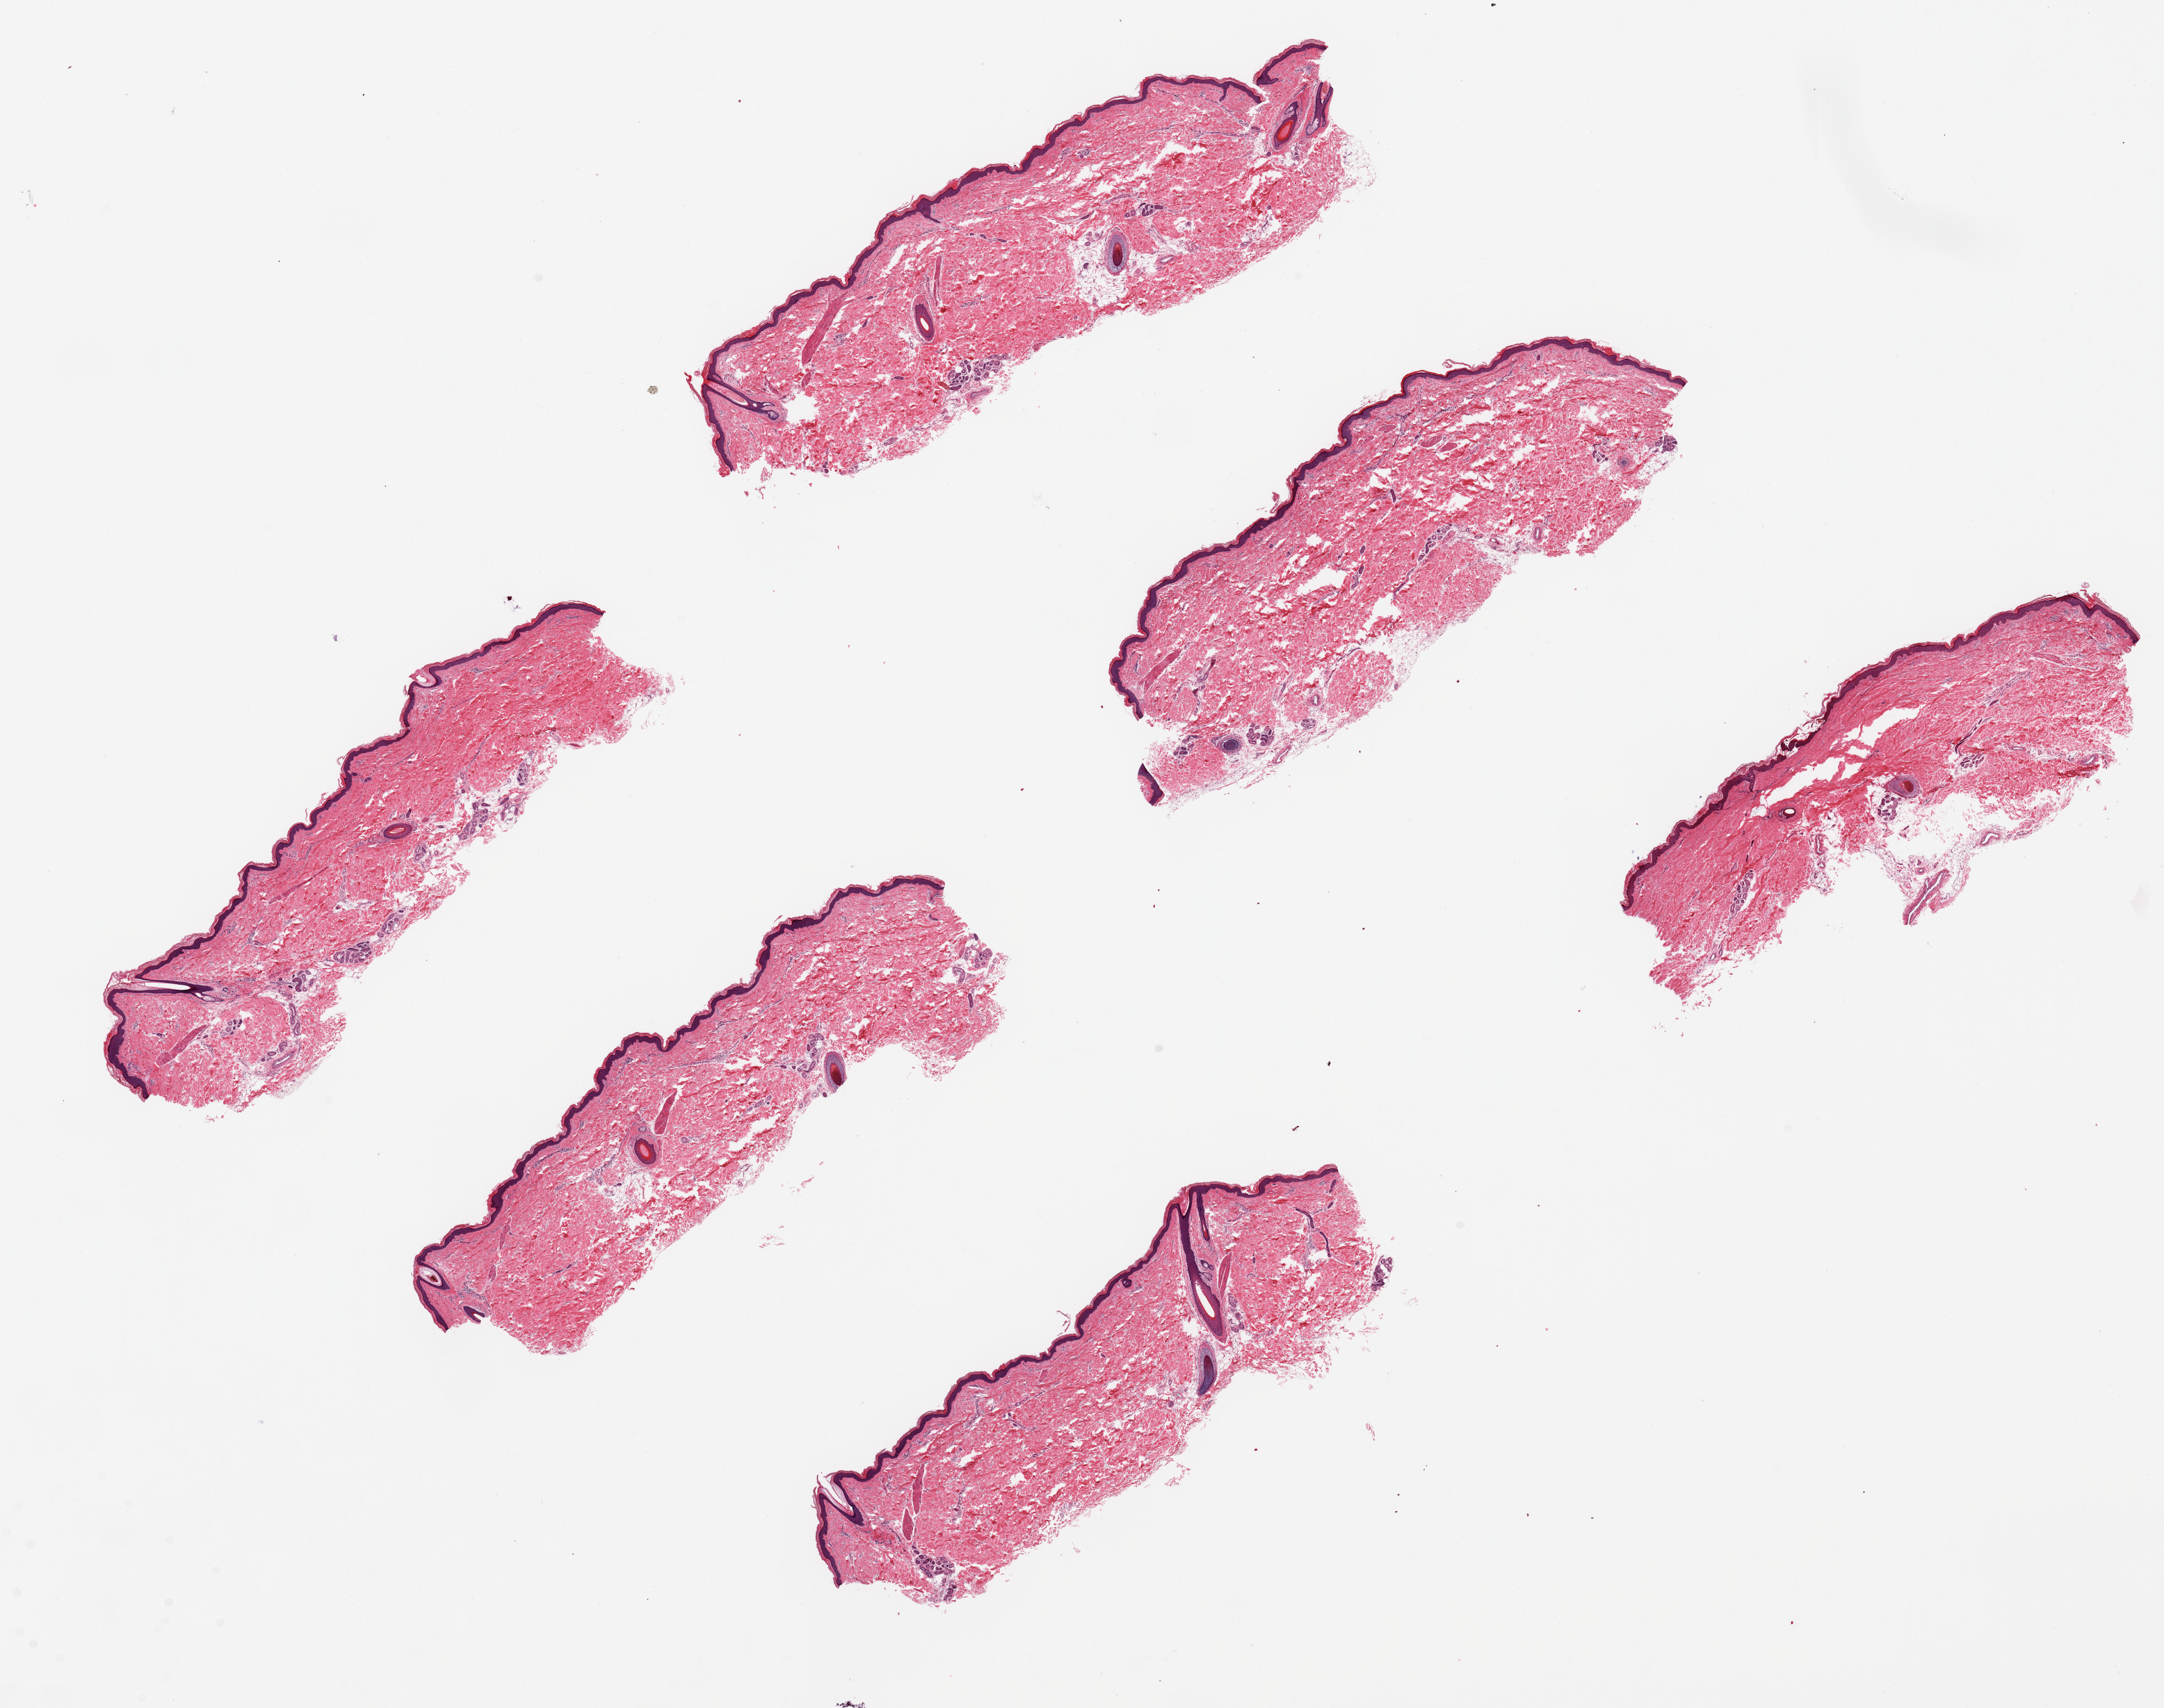
Whole-slide image, hematoxylin and eosin (H&E) stain, shown as a low-resolution overview of the whole scanned area (about 24.6 x 19.4 mm), PAXgene-fixed paraffin-embedded (PFPE) section, sampled site (target tissue): skin of lower leg, tissue donor sample. Donor: male.
Review note (as recorded): 6 pieces, ~8x2.5mm; good appendages.